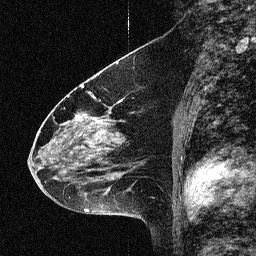
Breast MRI (dynamic contrast-enhanced), one sagittal slice. Dynamic contrast-enhanced study with each time point stored as its own series, time point 2 of 3 at this slice position (early post-contrast, ordered by acquisition time). 1.5 T. TE 4.5 ms, TR 11 ms. 2.06 mm slice thickness. 256 × 256 image matrix, field of view 200 × 200 mm. Female patient, age 46 years. From the clinical record (not read from this slice): setting: breast cancer imaged before/during neoadjuvant chemotherapy; receptor status: HER2-positive.
Structures marked on this image (semi-automatically segmented with operator editing):
- analysis volume of interest (the breast-tissue region the enhancement analysis was run in; not a lesion): bounding box (x1, y1, x2, y2) in pixels: (42, 80, 150, 180)
- tumour enhancement mask (voxels above the 90 % enhancement threshold inside the analysis volume of interest): (53, 85, 121, 180)